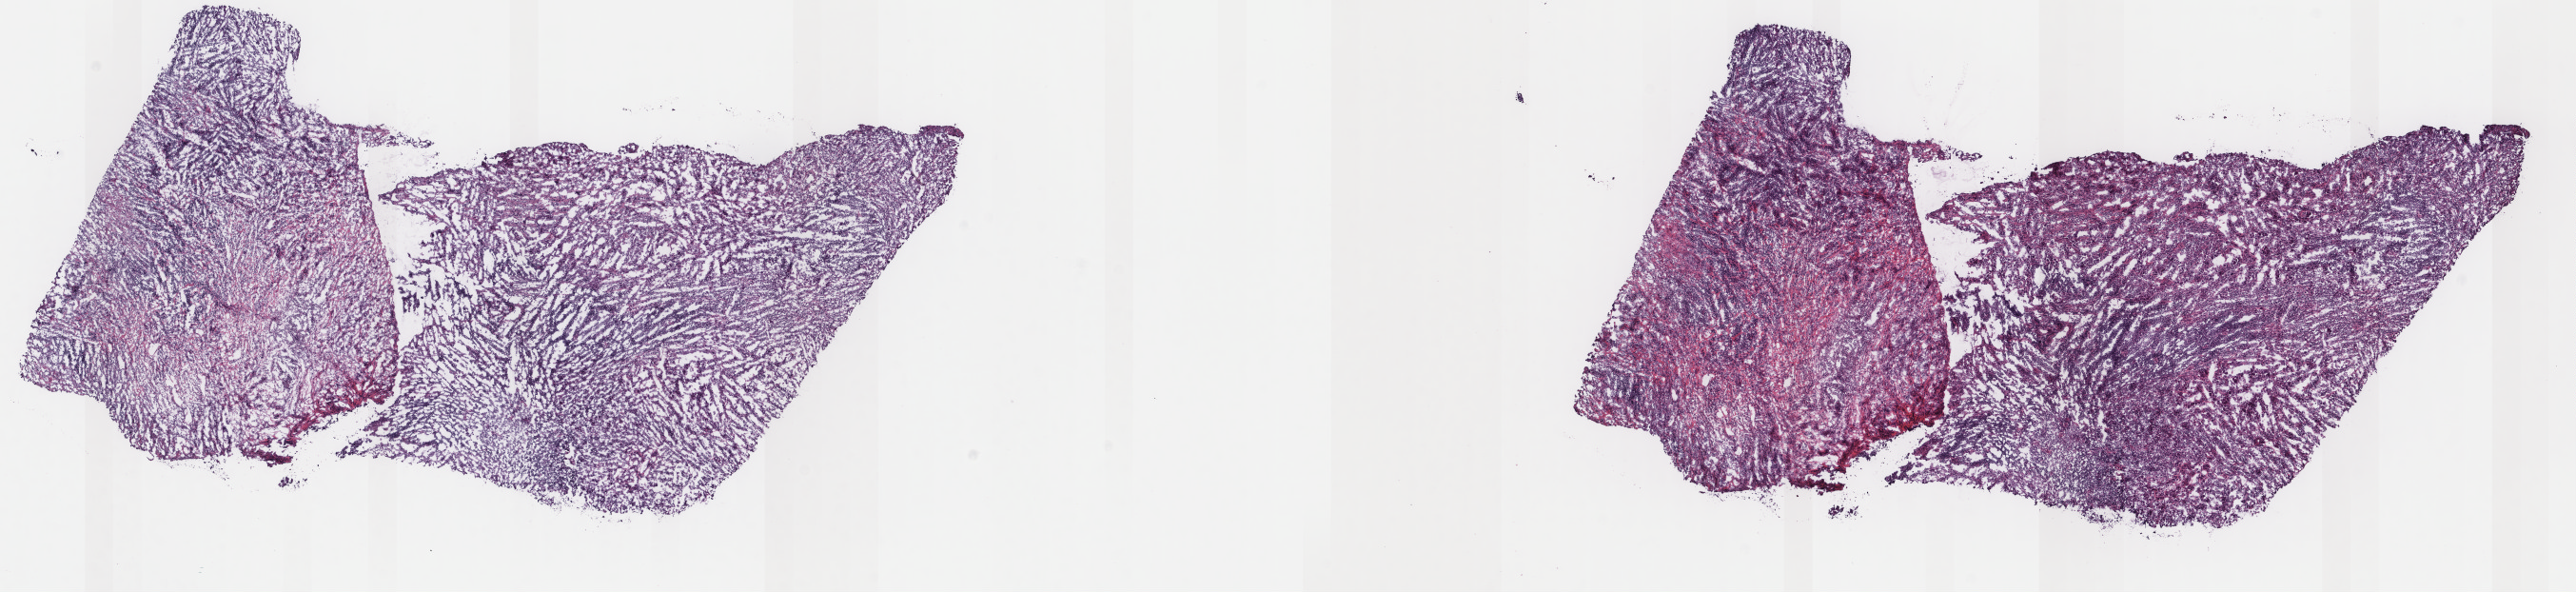
Hematoxylin and eosin (H&E) stained whole-slide image — shown as a low-resolution overview of the whole scanned area (about 21.5 x 4.9 mm, acquisition: 40x scan), frozen section from the top of the tissue portion, metastatic tumour sample, sampled site not recorded. Patient: female, age at initial diagnosis 69 years. Pathologist review of this section (percent, as recorded): tumour cells 100%, tumour nuclei 85%, normal cells 0%, stromal cells 0%, necrosis 0%. Inflammatory infiltration, as recorded: lymphocyte infiltration 0%, monocyte infiltration 0%, neutrophil infiltration 0%.
This section: metastatic tumour tissue. Patient diagnosis: Malignant melanoma, NOS.